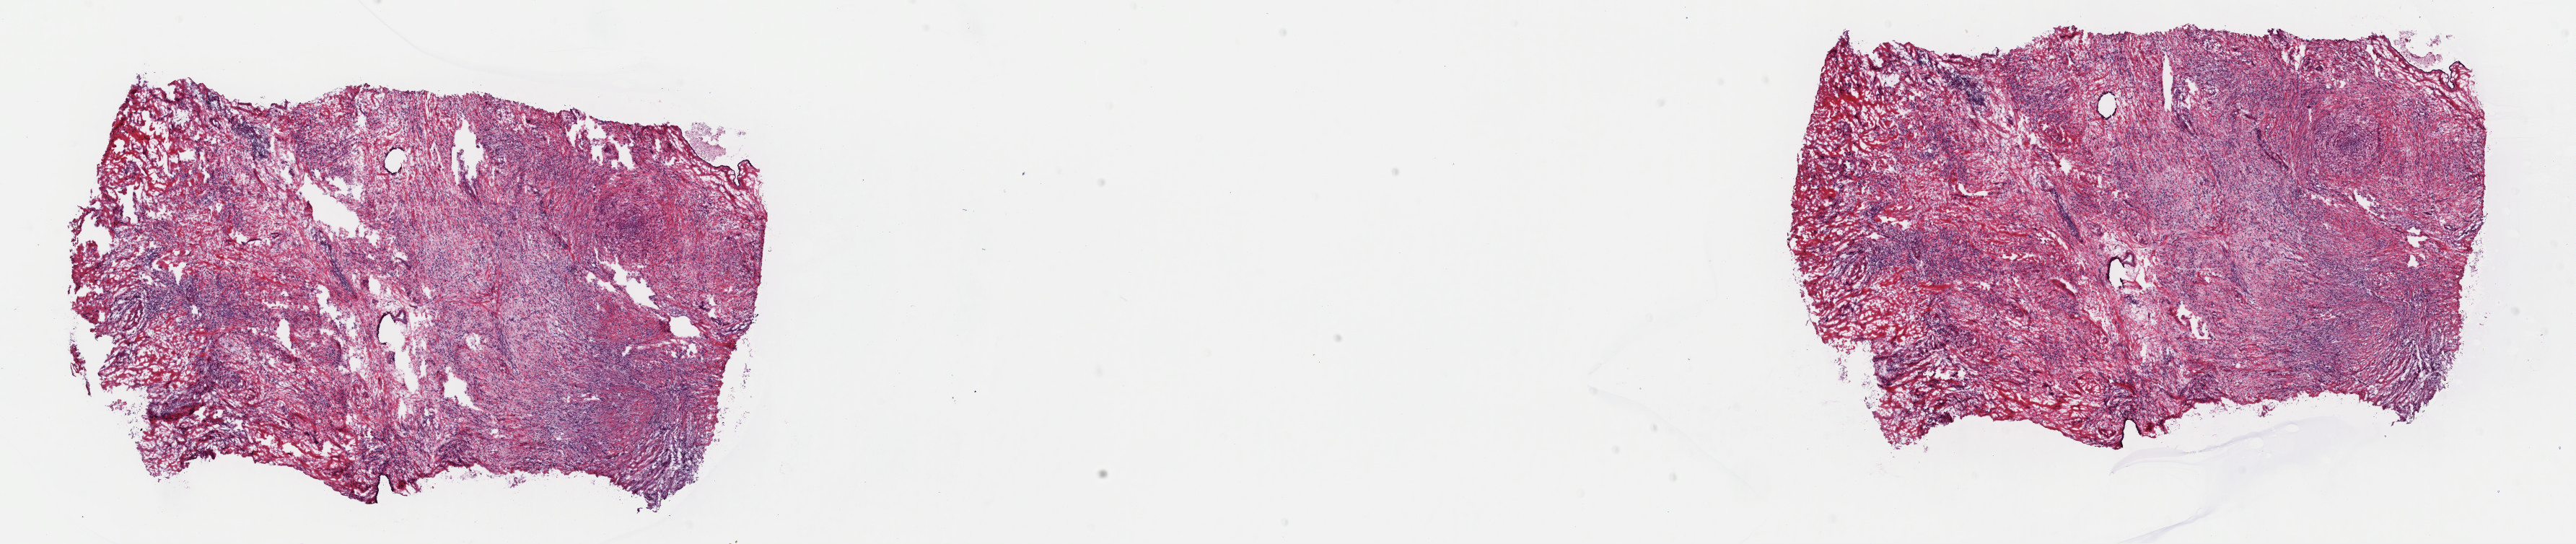
Whole-slide histology image, H&E-stained, a low-resolution overview of the entire scanned area, about 28.2 x 6.0 mm. Frozen section. Breast, primary tumour sample. Patient sex: female. Pathologist review of this section (percent, as recorded): tumour cells 95%, tumour nuclei 80%, normal cells 0%, stromal cells 5%, necrosis 0%. Infiltration values recorded for this section: lymphocyte infiltration 0%, monocyte infiltration 0%, neutrophil infiltration 0%.
* AJCC pathologic stage: IIIA (7th edition)
* histologic diagnosis: Lobular carcinoma, NOS